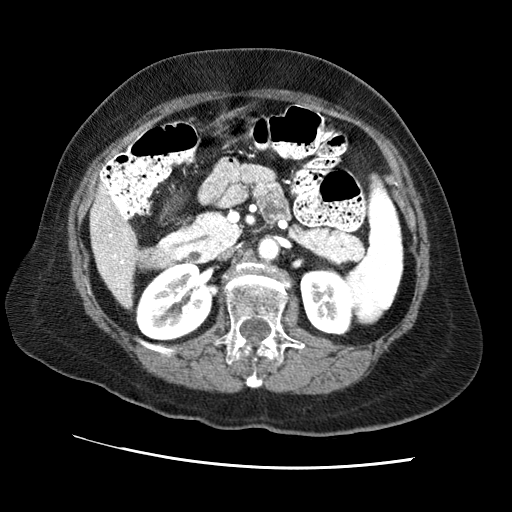
Contrast-enhanced abdominal CT (liver protocol), one axial slice; slice 20 of 65 in the series (ordered by position); reconstruction kernel STANDARD; 120 kVp; soft-tissue window (W 400 / L 40 HU); 2.5 mm slice thickness; 512 × 512 image matrix. From the clinical record (not read from this slice): diagnosis: hepatocellular carcinoma (patient treated with transarterial chemoembolisation; whether this scan precedes or follows treatment is not stated here); TNM stage (as recorded): Stage-II; Child-Pugh class: A; tumour differentiation: no biopsy; tumour nodularity: multinodular.
Structures marked on this image (semi-automatic segmentation, software-assisted and operator-edited):
- liver parenchyma outside the tumour (the mass and vessels are separate outlines, so this box may not span the whole liver): bounding box <90,190,136,306> (left, top, right, bottom; pixels)
- liver vessels: <93,192,128,292>